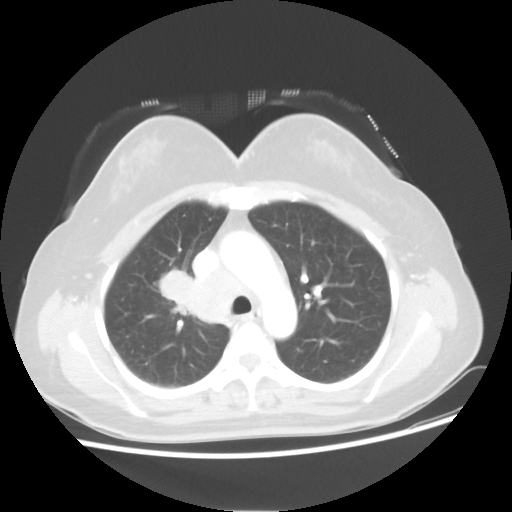
Chest CT, one axial slice; slice 35 of 50 in the series (ordered by position); lung window (W 1500 / L -600 HU); 5 mm slice thickness; 512 × 512 image matrix, field of view 360 × 360 mm. Female patient, age 40 years. Case-level facts recorded for this patient, not image findings: clinical TNM (as recorded): T1c N3 M0; histopathological grade: G3.
Annotated regions visible in this slice (bounding box drawn by a radiologist):
- lung tumour (recorded histology: small cell carcinoma): bounding box (x1, y1, x2, y2) in pixels: (156, 265, 191, 312)